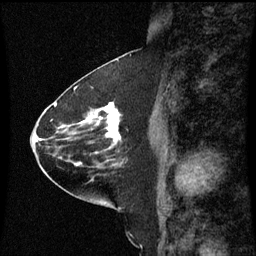
Breast MRI (dynamic contrast-enhanced), one sagittal slice. Position 30 of 60 along the scan axis. Dynamic contrast-enhanced series, image 2 of 3 at this slice position (ordered by acquisition). 1.5 T. TE 4.2 ms, TR 8.9 ms. 256 × 256 image matrix, field of view 200 × 200 mm. Patient: female, 63 years. Case-level facts recorded for this patient, not image findings: setting: breast cancer imaged before/during neoadjuvant chemotherapy; receptor status: HR-positive, HER2-negative.
Structures marked on this image (semi-automatically segmented with operator editing):
- analysis volume of interest (the breast-tissue region the enhancement analysis was run in; not a lesion): bounding box (x1, y1, x2, y2) in pixels: (77, 102, 123, 151)
- tumour enhancement mask (voxels above the 70 % enhancement threshold inside the analysis volume of interest): (84, 102, 120, 141)